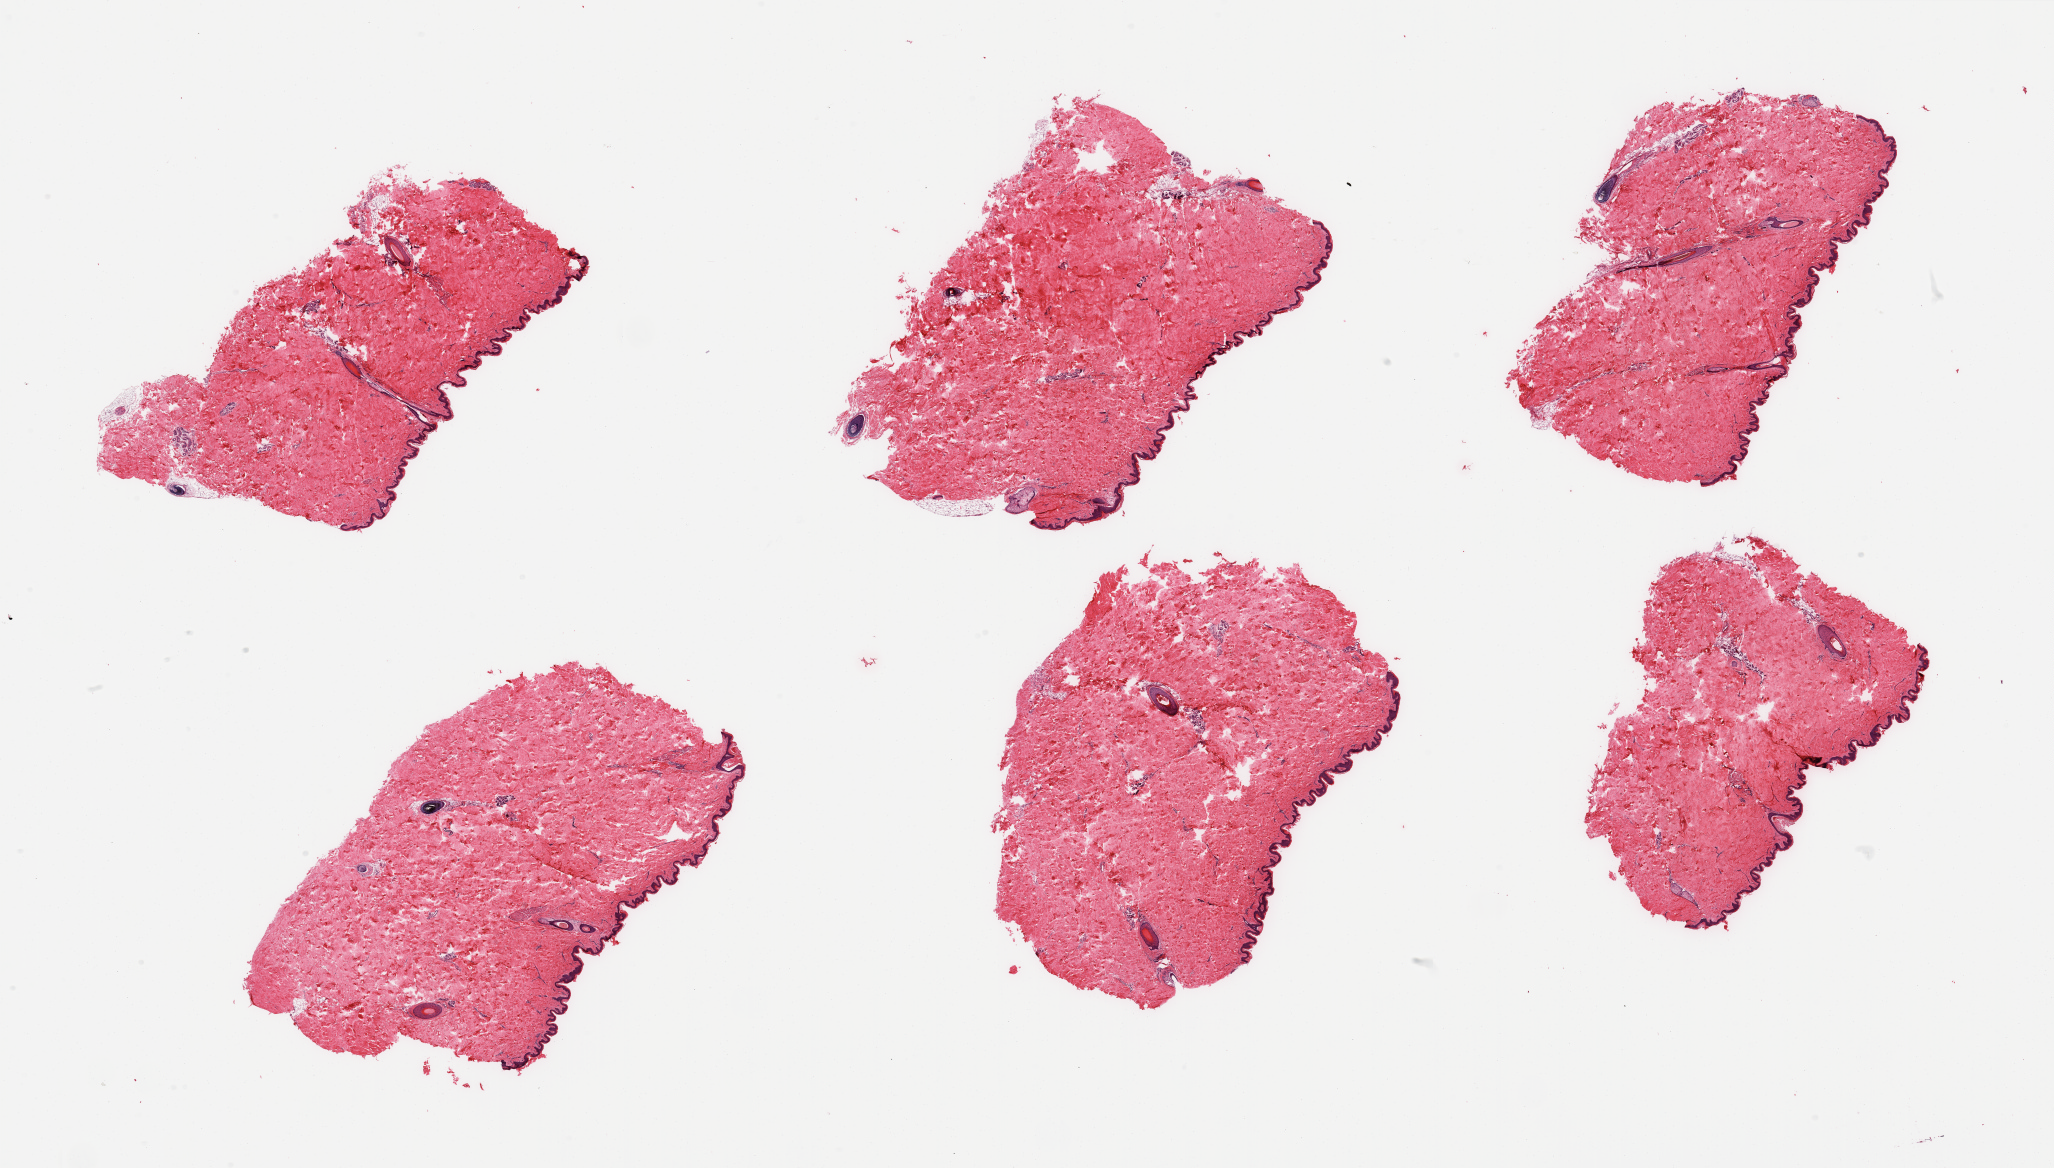
Digitized hematoxylin and eosin (H&E)-stained section, brightfield, low-resolution overview of the scanned area, about 32.5 x 18.5 mm. PAXgene-fixed paraffin-embedded (PFPE) section. Section of skin of suprapubic region (target tissue). Tissue donor sample. Donor sex: male.
- review note (as recorded): 6 pieces, no significant dermal fat; squamous epithelium is 30-40 microns